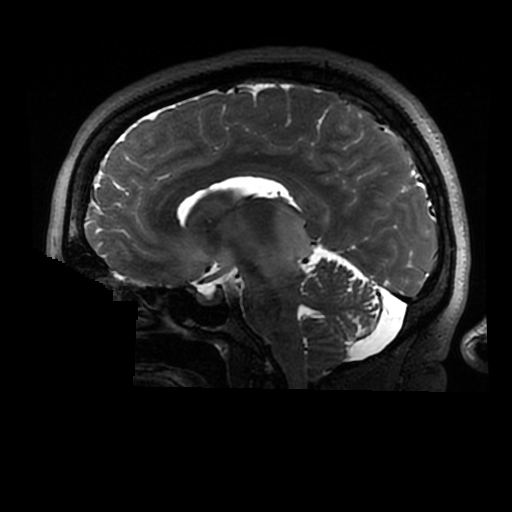
Brain MRI from a brain-tumour surgery series, one sagittal slice. 0.6 mm slice thickness. 512 × 512 image matrix, field of view 240 × 240 mm. Case-level facts recorded for this patient, not image findings: histopathology: Astrocytoma; WHO grade: 2; IDH mutation: yes.
Annotated regions visible in this slice (expert manual segmentation):
- tumour: box from (x=271, y=203) to (x=314, y=267) px